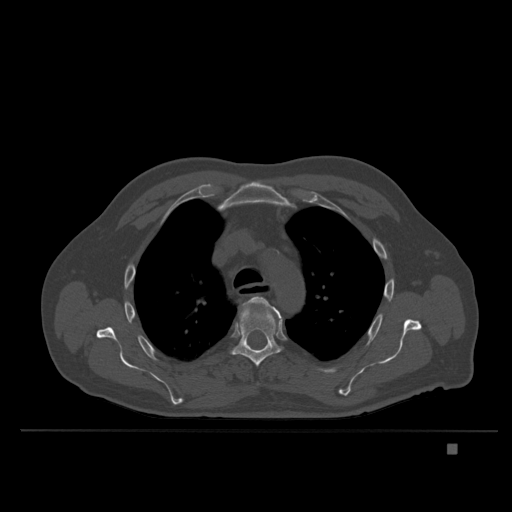
CT including the spine, one axial slice. Position 276 of 435 along the scan axis. Bone window (W 1800 / L 400 HU). 1.5 mm slice thickness. 512 × 512 image matrix, field of view 434 × 434 mm. Male patient, age 73 years. From the clinical record (not read from this slice): primary cancer: skin.
Annotated regions visible in this slice (semi-automatic segmentation, software-assisted and operator-edited):
- T4 vertebra: bounding box <242,296,270,308> (left, top, right, bottom; pixels)
- T5 vertebra: <230,298,284,367>